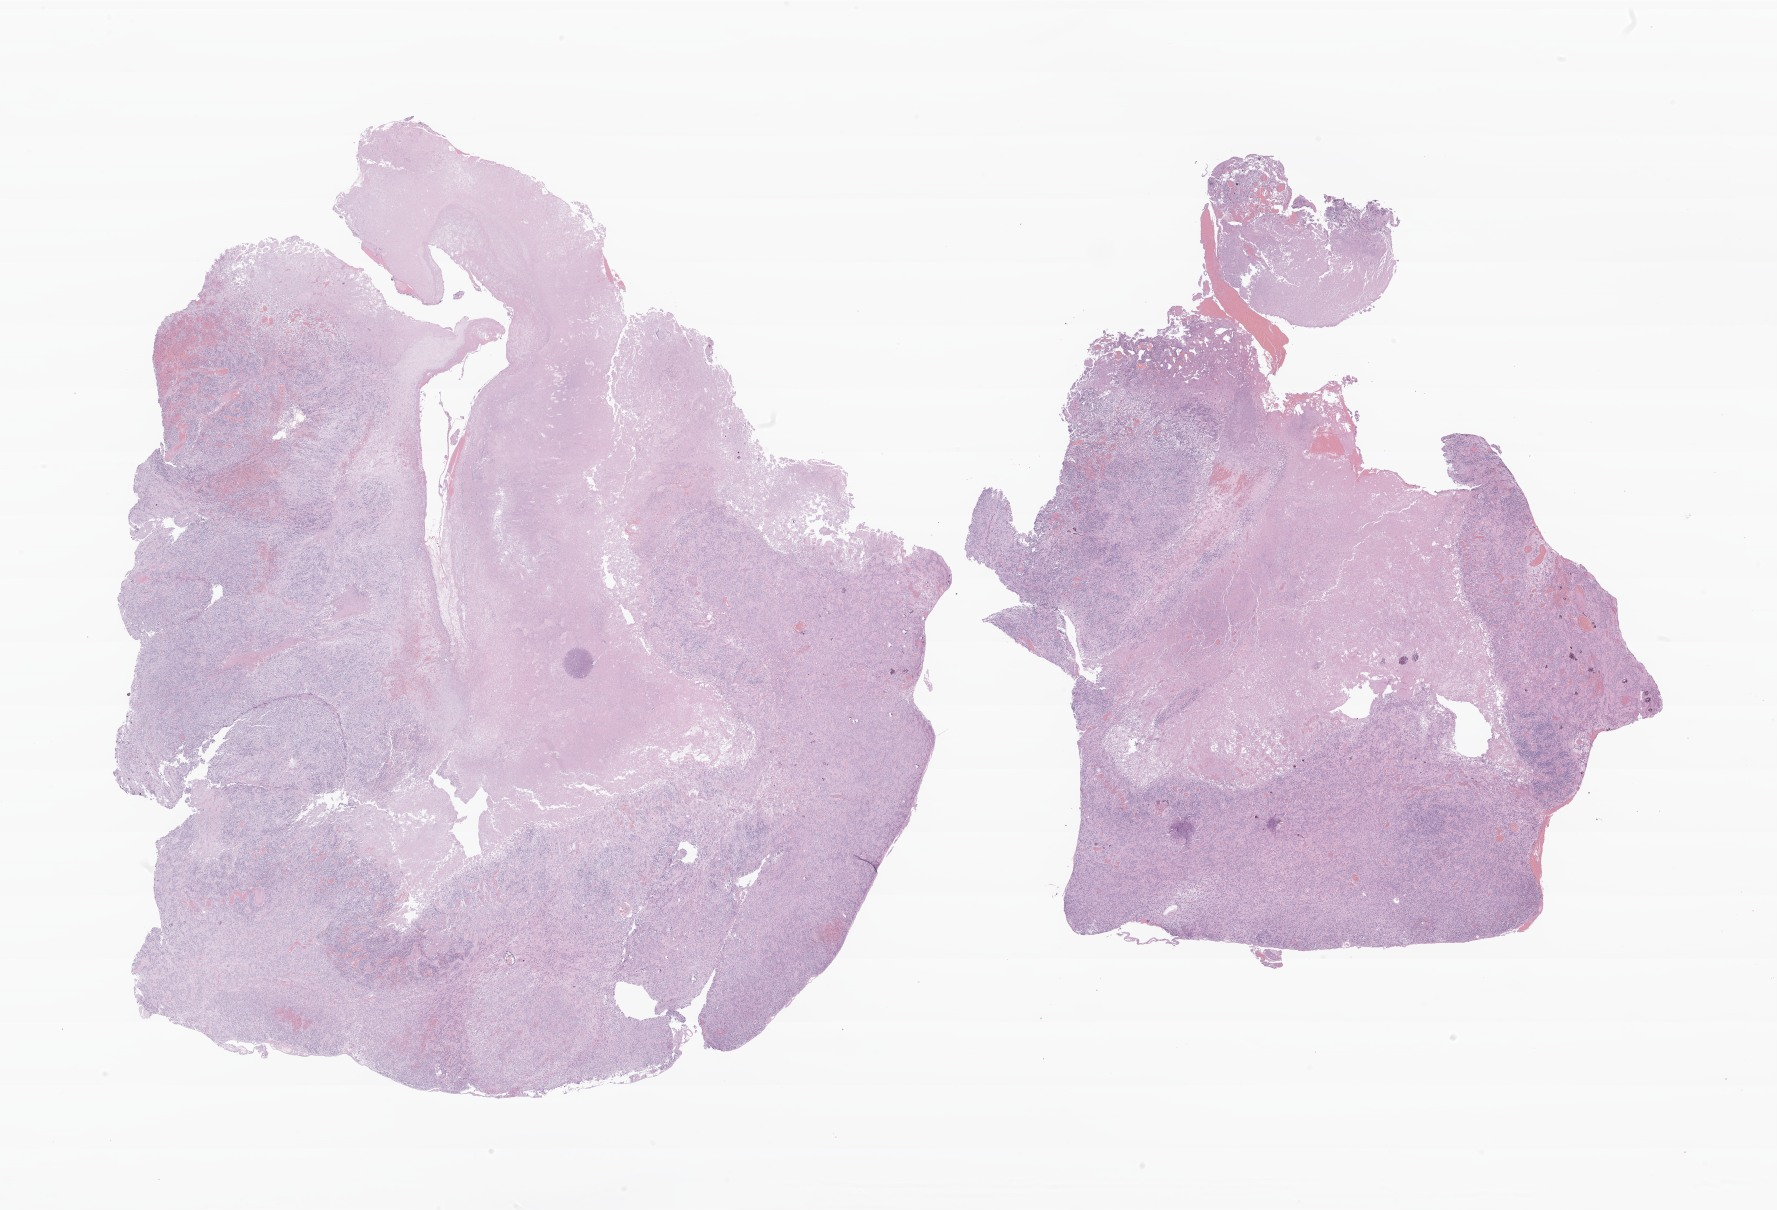
Haematoxylin and eosin whole-slide image of tumor tissue from the brain, whole scanned area (about 29.9 x 20.4 mm) shown as a low-resolution overview; formalin-fixed paraffin-embedded section. Patient female; age 584 days.
Diagnosis: Ependymoma, NOS.